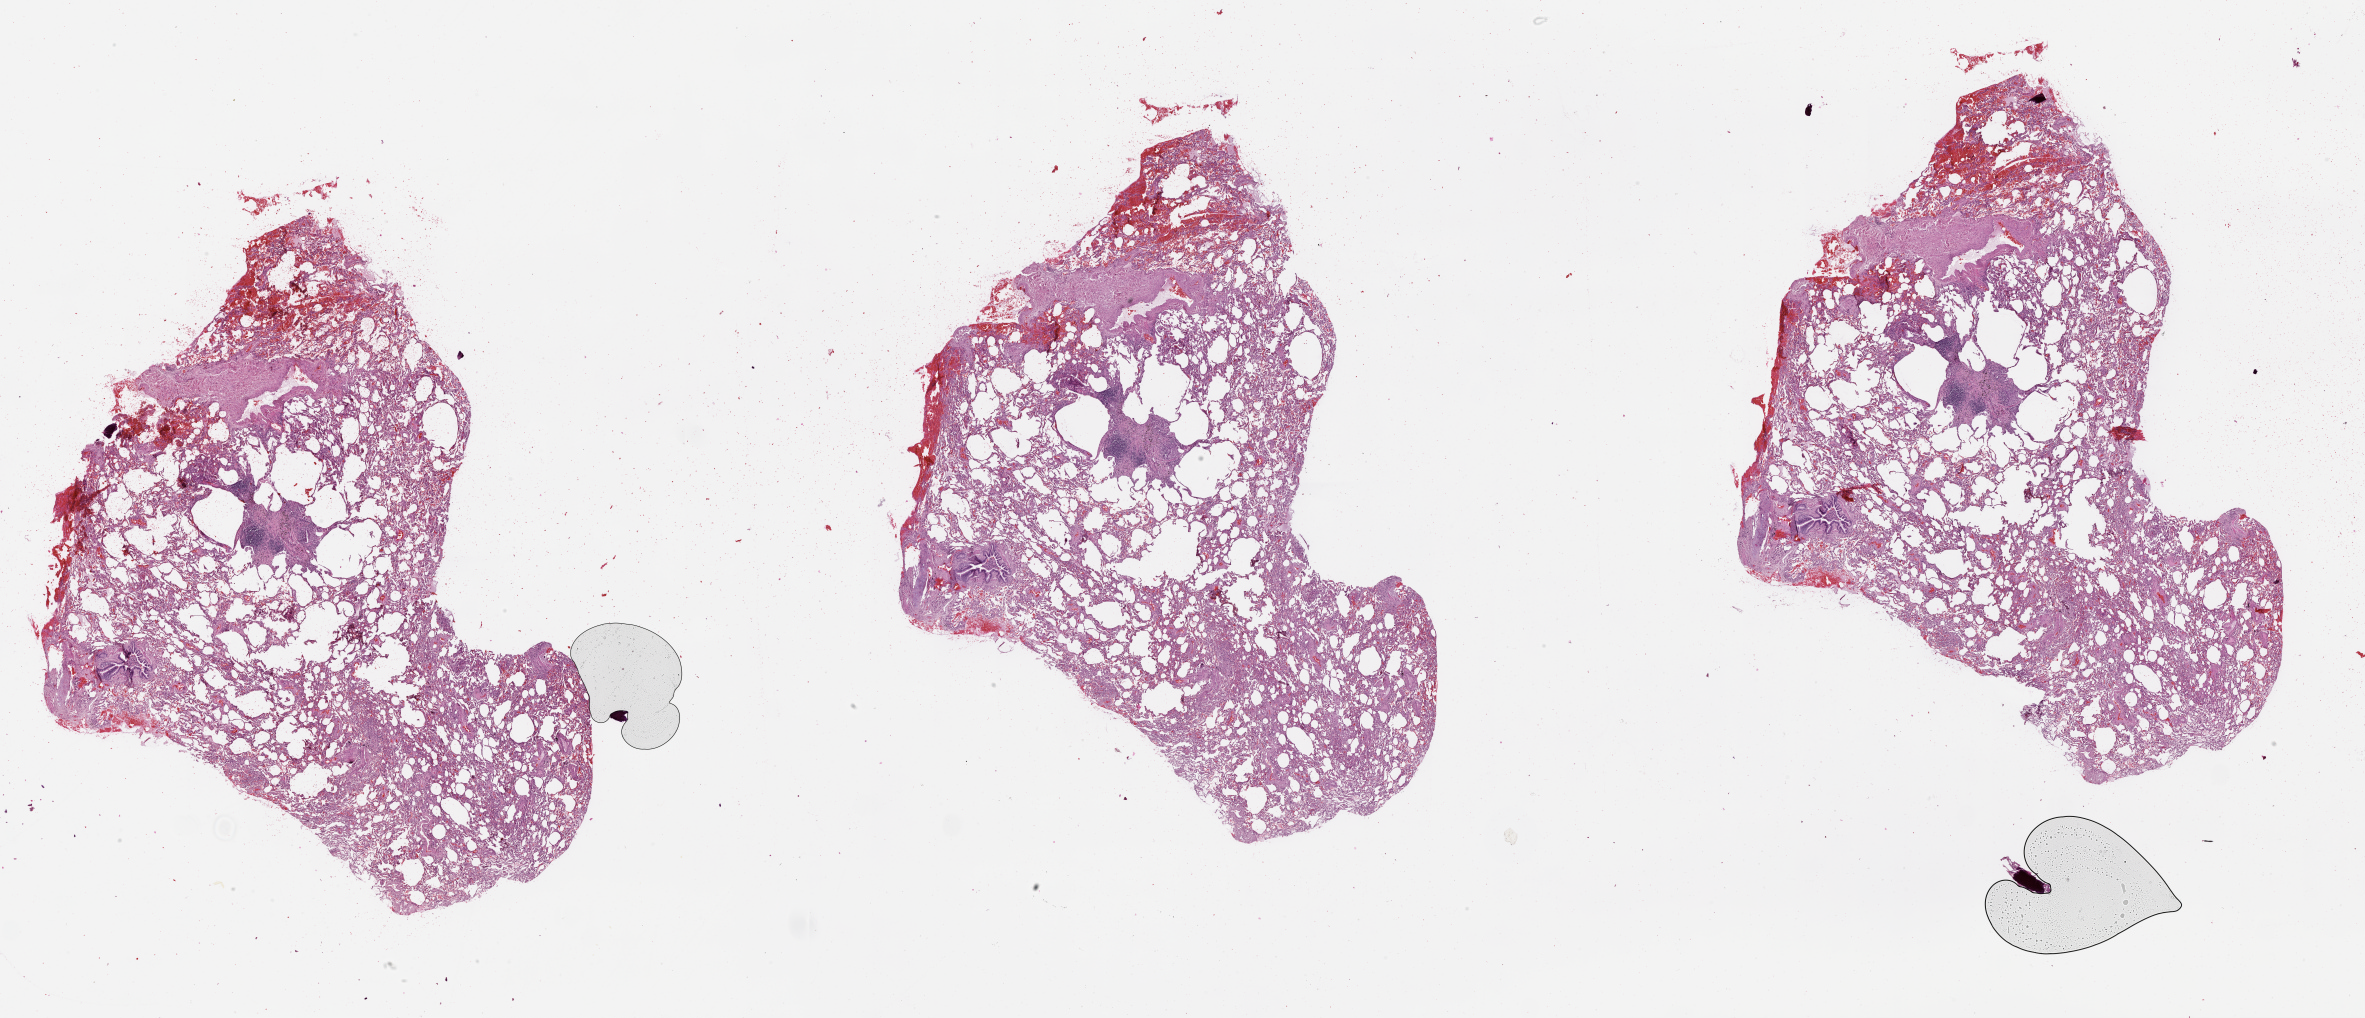
Whole-slide histology image, H&E — whole scanned area (about 38.1 x 16.4 mm) shown as a low-resolution overview. Lung, normal (non-tumour) tissue. 58-year-old male patient.
This section: normal (non-tumour) tissue from the same patient. Patient diagnosis (cohort enrolment): squamous cell carcinoma (lung).